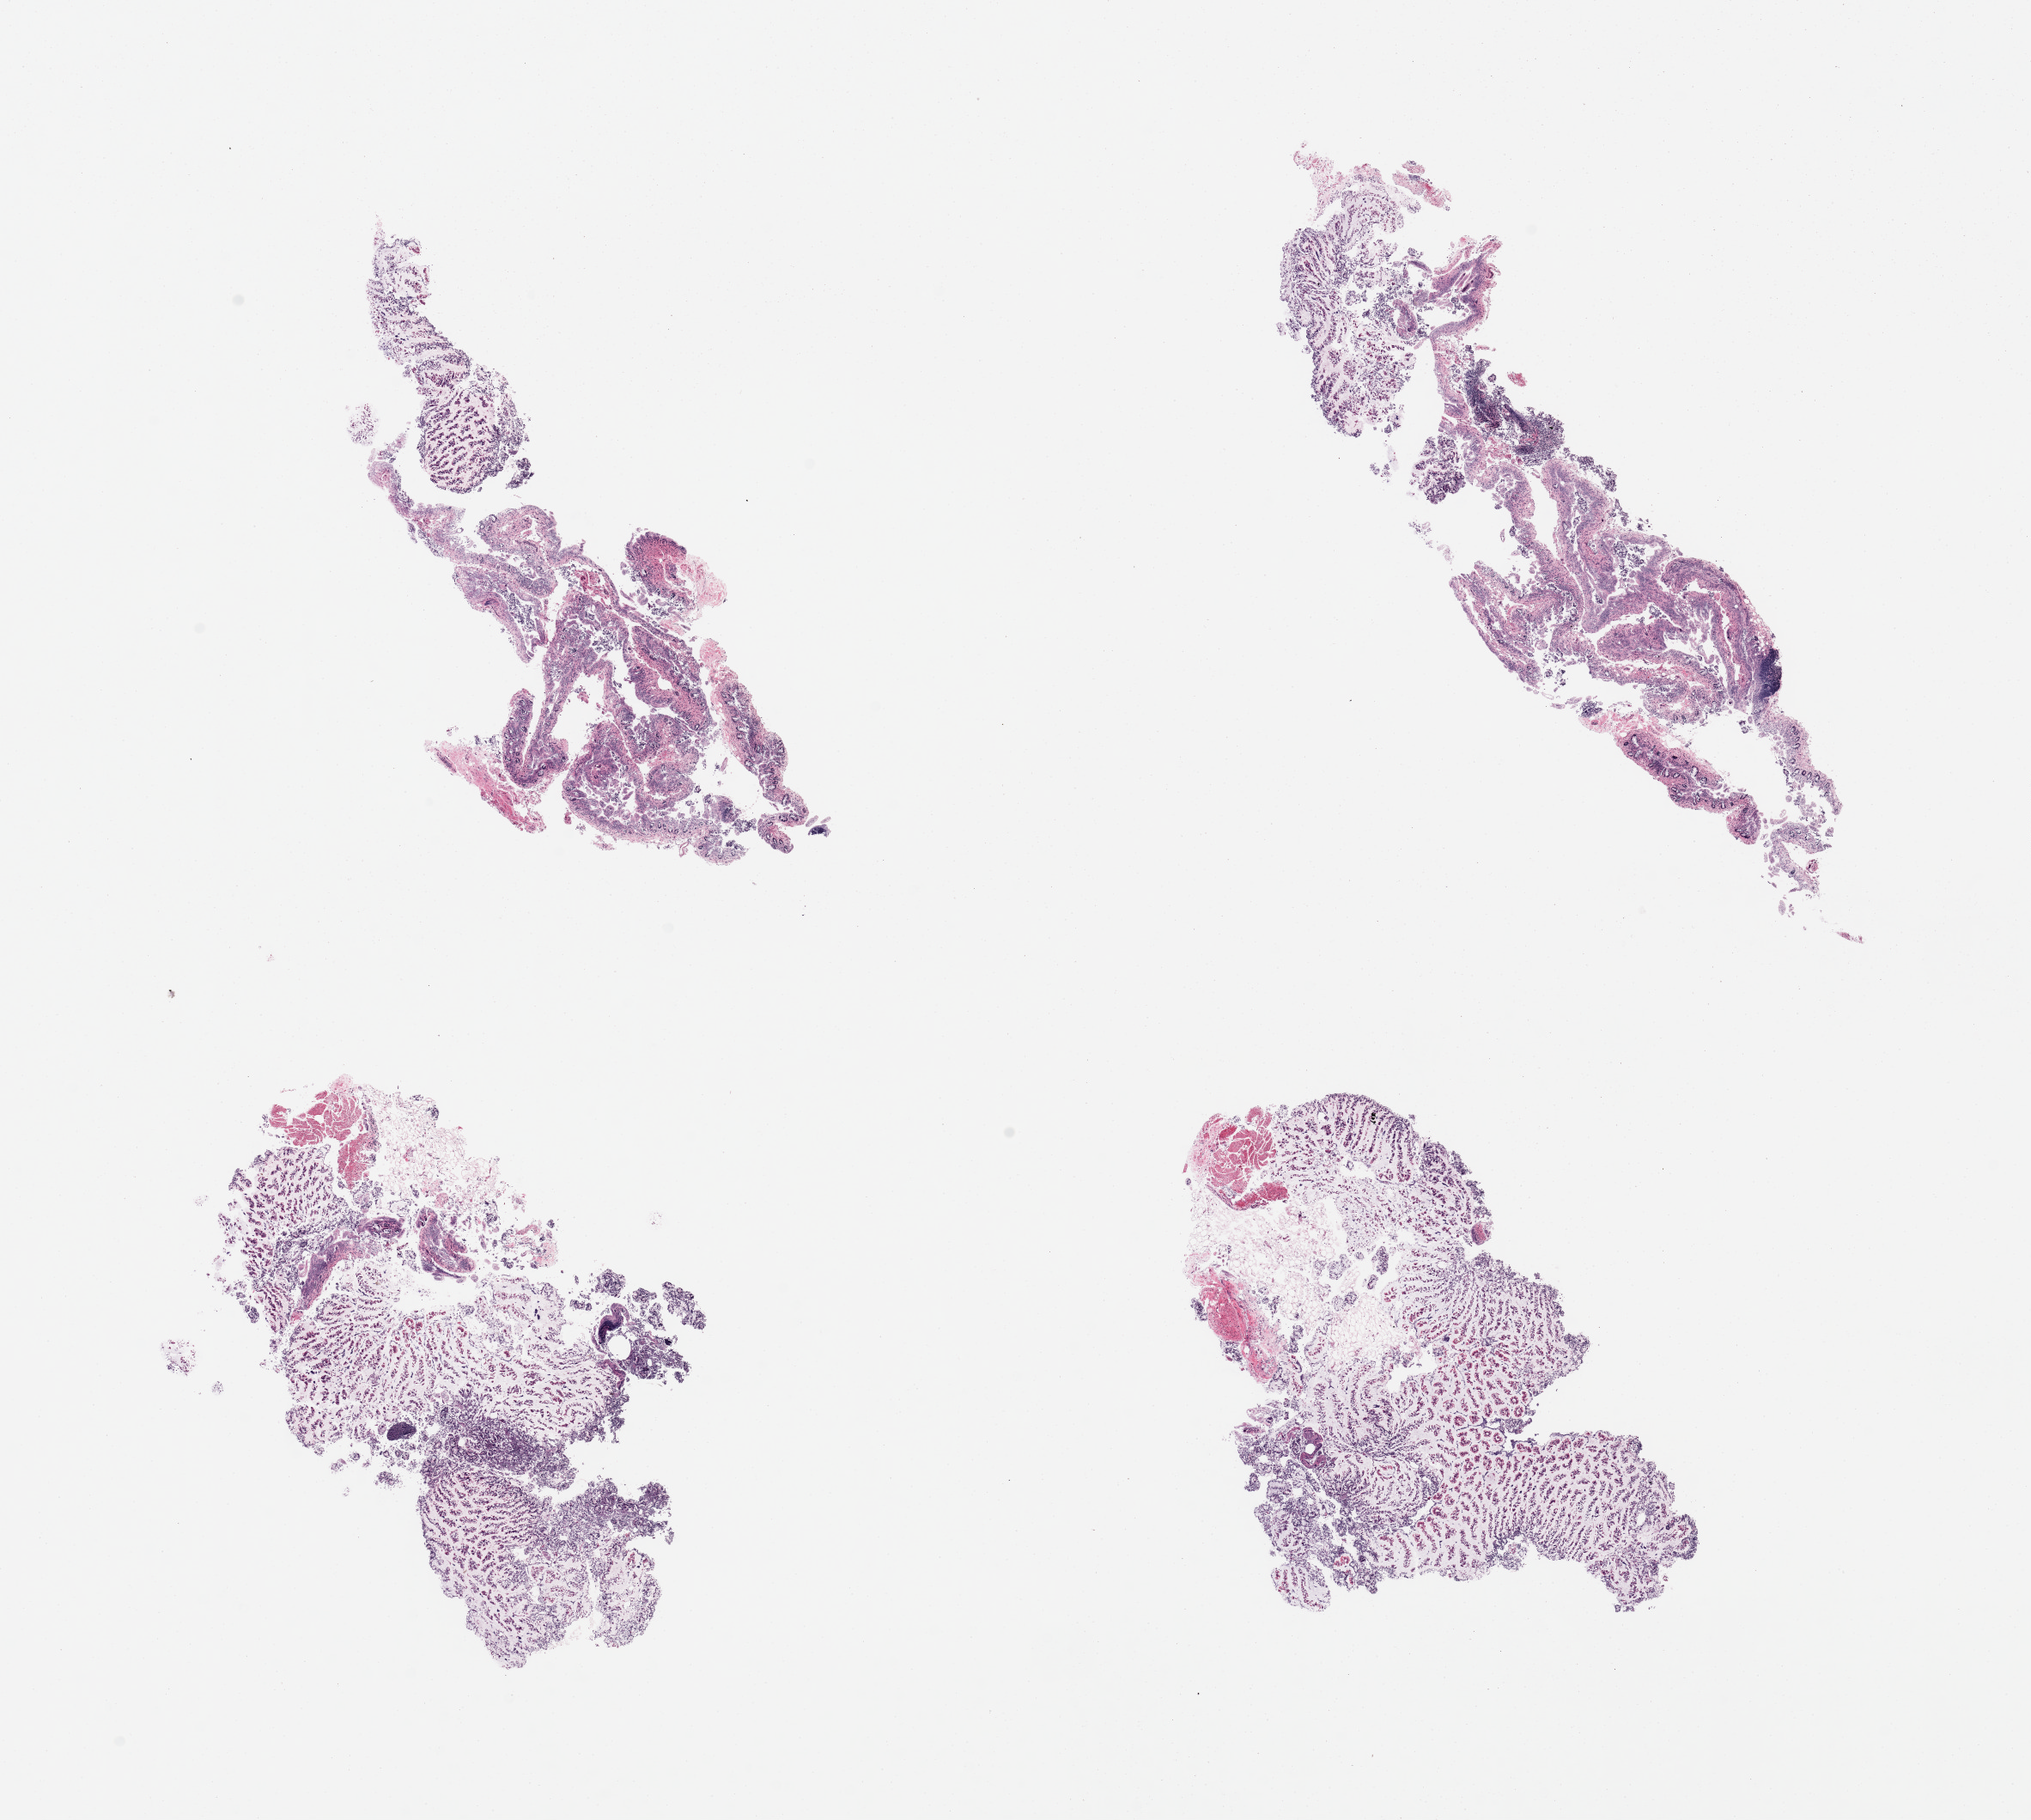
Whole-slide image, H&E stain, brightfield, whole scanned area (about 18.7 x 16.8 mm) shown as a low-resolution overview; PAXgene-fixed, paraffin-embedded tissue; sampled site (target tissue): ileum; tissue donor sample.
• reviewer comment on this tissue sample: 4 pieces; 2 minute autolyzed lymphoid collections